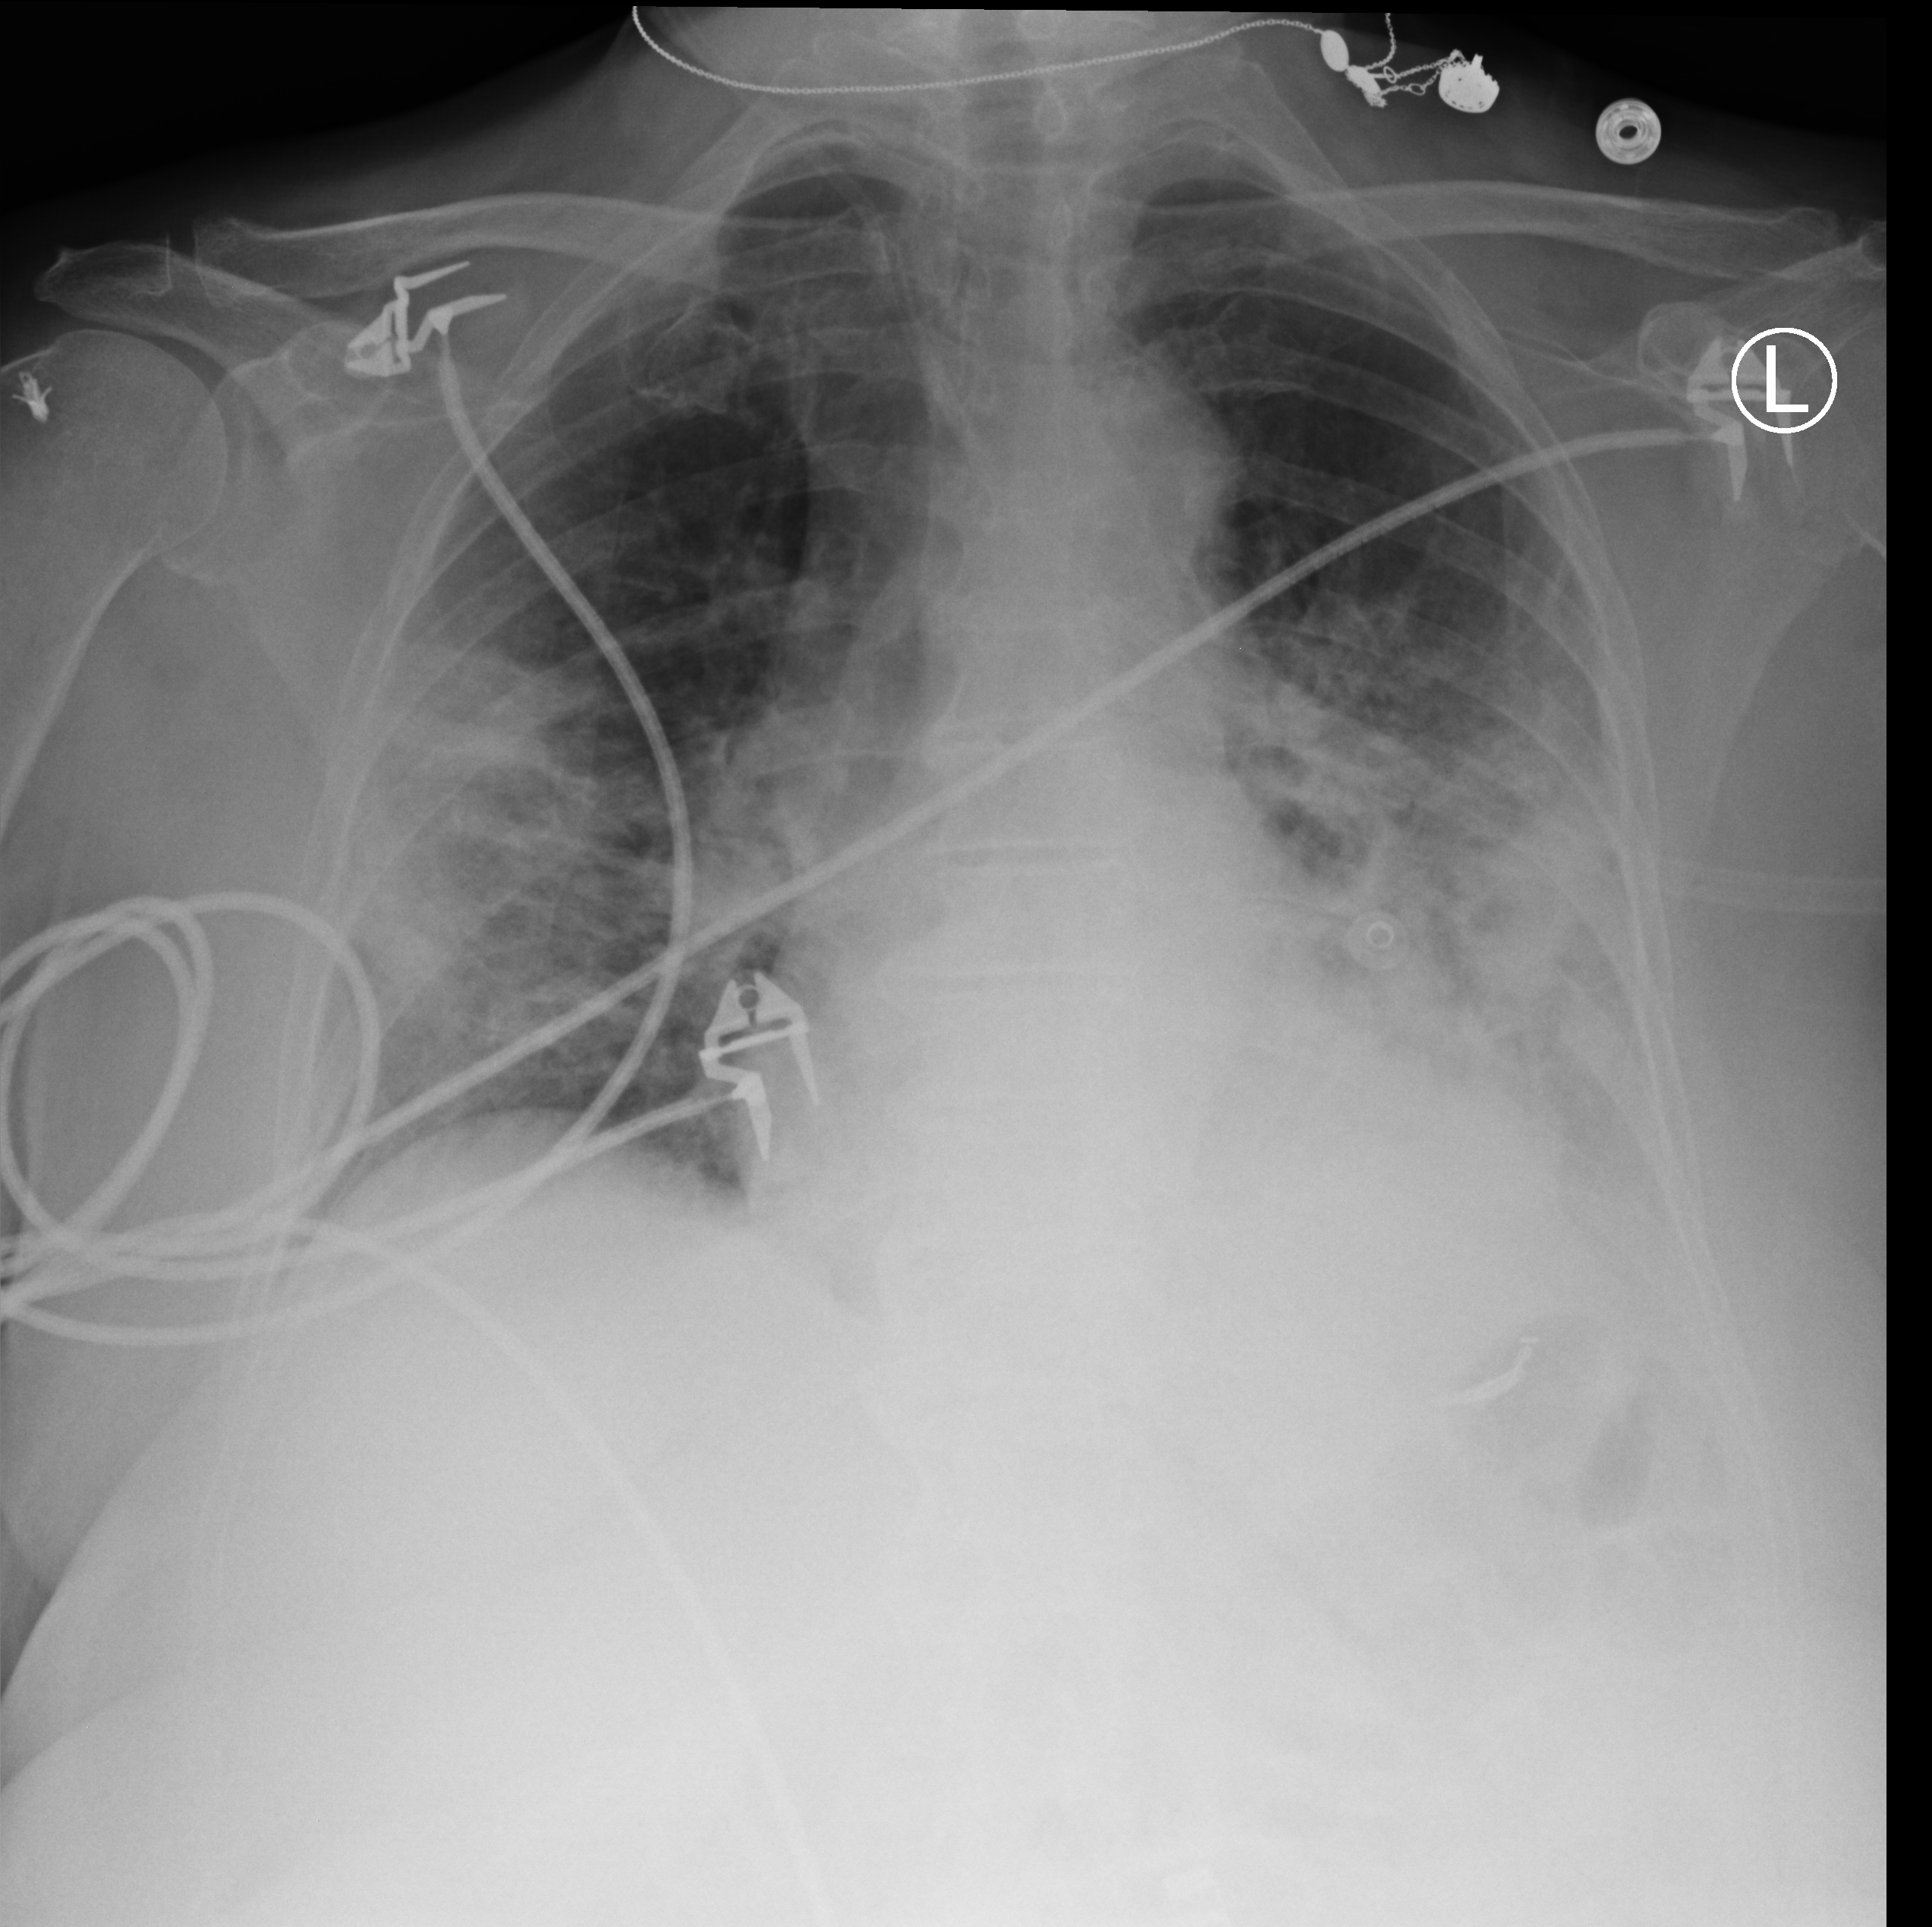
Chest X-ray (portable), anteroposterior (AP) projection. Patient hospitalised with COVID-19; female, aged 60–74 years.
Hospital-stay facts (about this admission, not read from this image; timing relative to this image not recorded):
- admitted to intensive care during this hospital stay: no
- mechanically ventilated during this hospital stay: no